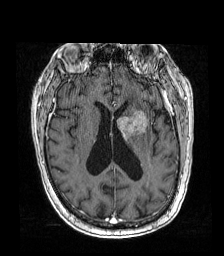
Brain MRI from a brain-tumour surgery series, one axial slice; position 76 of 192 along the scan axis; T1-weighted post-contrast; 1 mm slice thickness; 224 × 256 image matrix, field of view 219 × 250 mm. Case-level facts recorded for this patient, not image findings: histopathology: Metastatic carcinoma from lung primary.
Annotated regions visible in this slice (manually delineated by an expert):
- tumour: box from (x=117, y=110) to (x=148, y=140) px